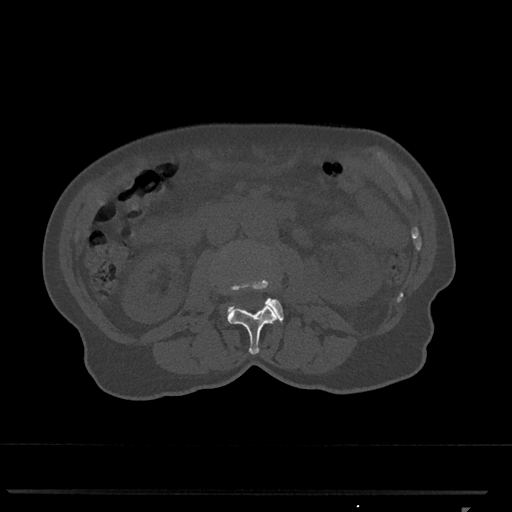
CT including the spine, one axial slice. Slice 309 of 793 in the series (ordered by position). Bone window (W 1800 / L 400 HU). 0.5 mm slice thickness. 512 × 512 image matrix, field of view 380 × 380 mm. Patient: female, 62 years. From the clinical record (not read from this slice): primary cancer: renal.
Structures marked on this image (semi-automatic segmentation, software-assisted and operator-edited):
- L2 vertebra: bounding box (x1, y1, x2, y2) in pixels: (227, 303, 278, 354)
- L3 vertebra: (226, 280, 284, 322)